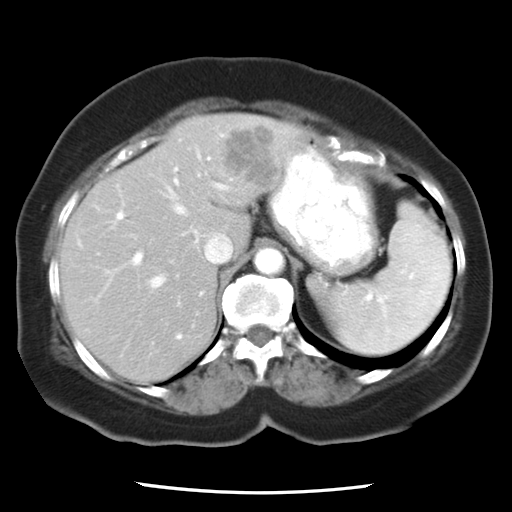
Contrast-enhanced abdominal CT, one axial slice; slice 17 of 24 in the series (ordered by position); reconstruction kernel STANDARD; intravenous contrast given; soft-tissue window (W 400 / L 40 HU); 512 × 512 image matrix. Female patient, age 71 years. Case-level facts recorded for this patient, not image findings: diagnosis: colorectal cancer liver metastases, imaged before liver resection; multiple liver metastases: no; largest metastasis: 4.3 cm; disease in both lobes: no.
Structures marked on this image (outlined manually by an expert reader):
- hepatic veins: bounding box (x1, y1, x2, y2) in pixels: (122, 185, 235, 290)
- liver: (59, 114, 306, 381)
- planned liver remnant (the part of the liver to remain after resection): (59, 130, 249, 381)
- portal vein (with intrahepatic branches): (113, 135, 233, 339)
- liver metastasis: (221, 123, 282, 190)